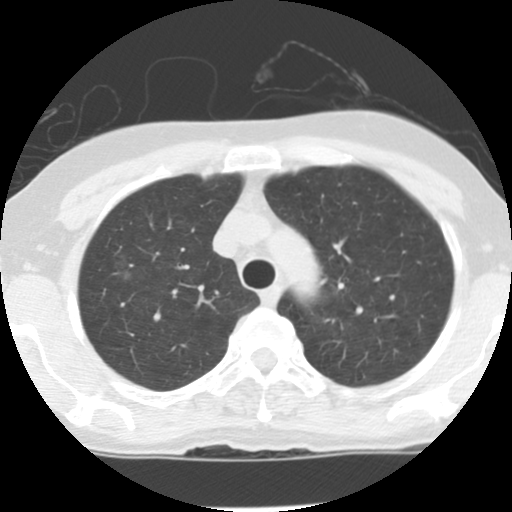
Chest CT (low-dose screening protocol), one axial image. Baseline screening round. Lung window (W 1500 / L -600 HU). 2.5 mm slice thickness. Standard (soft-tissue) reconstruction kernel (STANDARD). Slice 25 of 134 in the series. 512 × 512 image matrix. Female, age 62 years at enrolment.
Lesion marked by an expert reader, bounding box <105,252,144,293> (left, top, right, bottom; pixels). Screening reader's record for this exam (one nodule recorded; not confirmed to be the boxed lesion): non-calcified nodule or mass ≥4 mm, right upper lobe, 7 × 5 mm, poorly defined margins, ground glass attenuation. Official screen result: positive, change unspecified: nodule(s) >= 4 mm or enlarging nodule(s), mass(es), or other non-specific abnormalities suspicious for lung cancer. Participant outcome: lung cancer diagnosed 875 days after this screen — bronchiolo-alveolar adenocarcinoma, NOS, right upper lobe, stage IA (AJCC 6th edition), 10 mm at pathology.